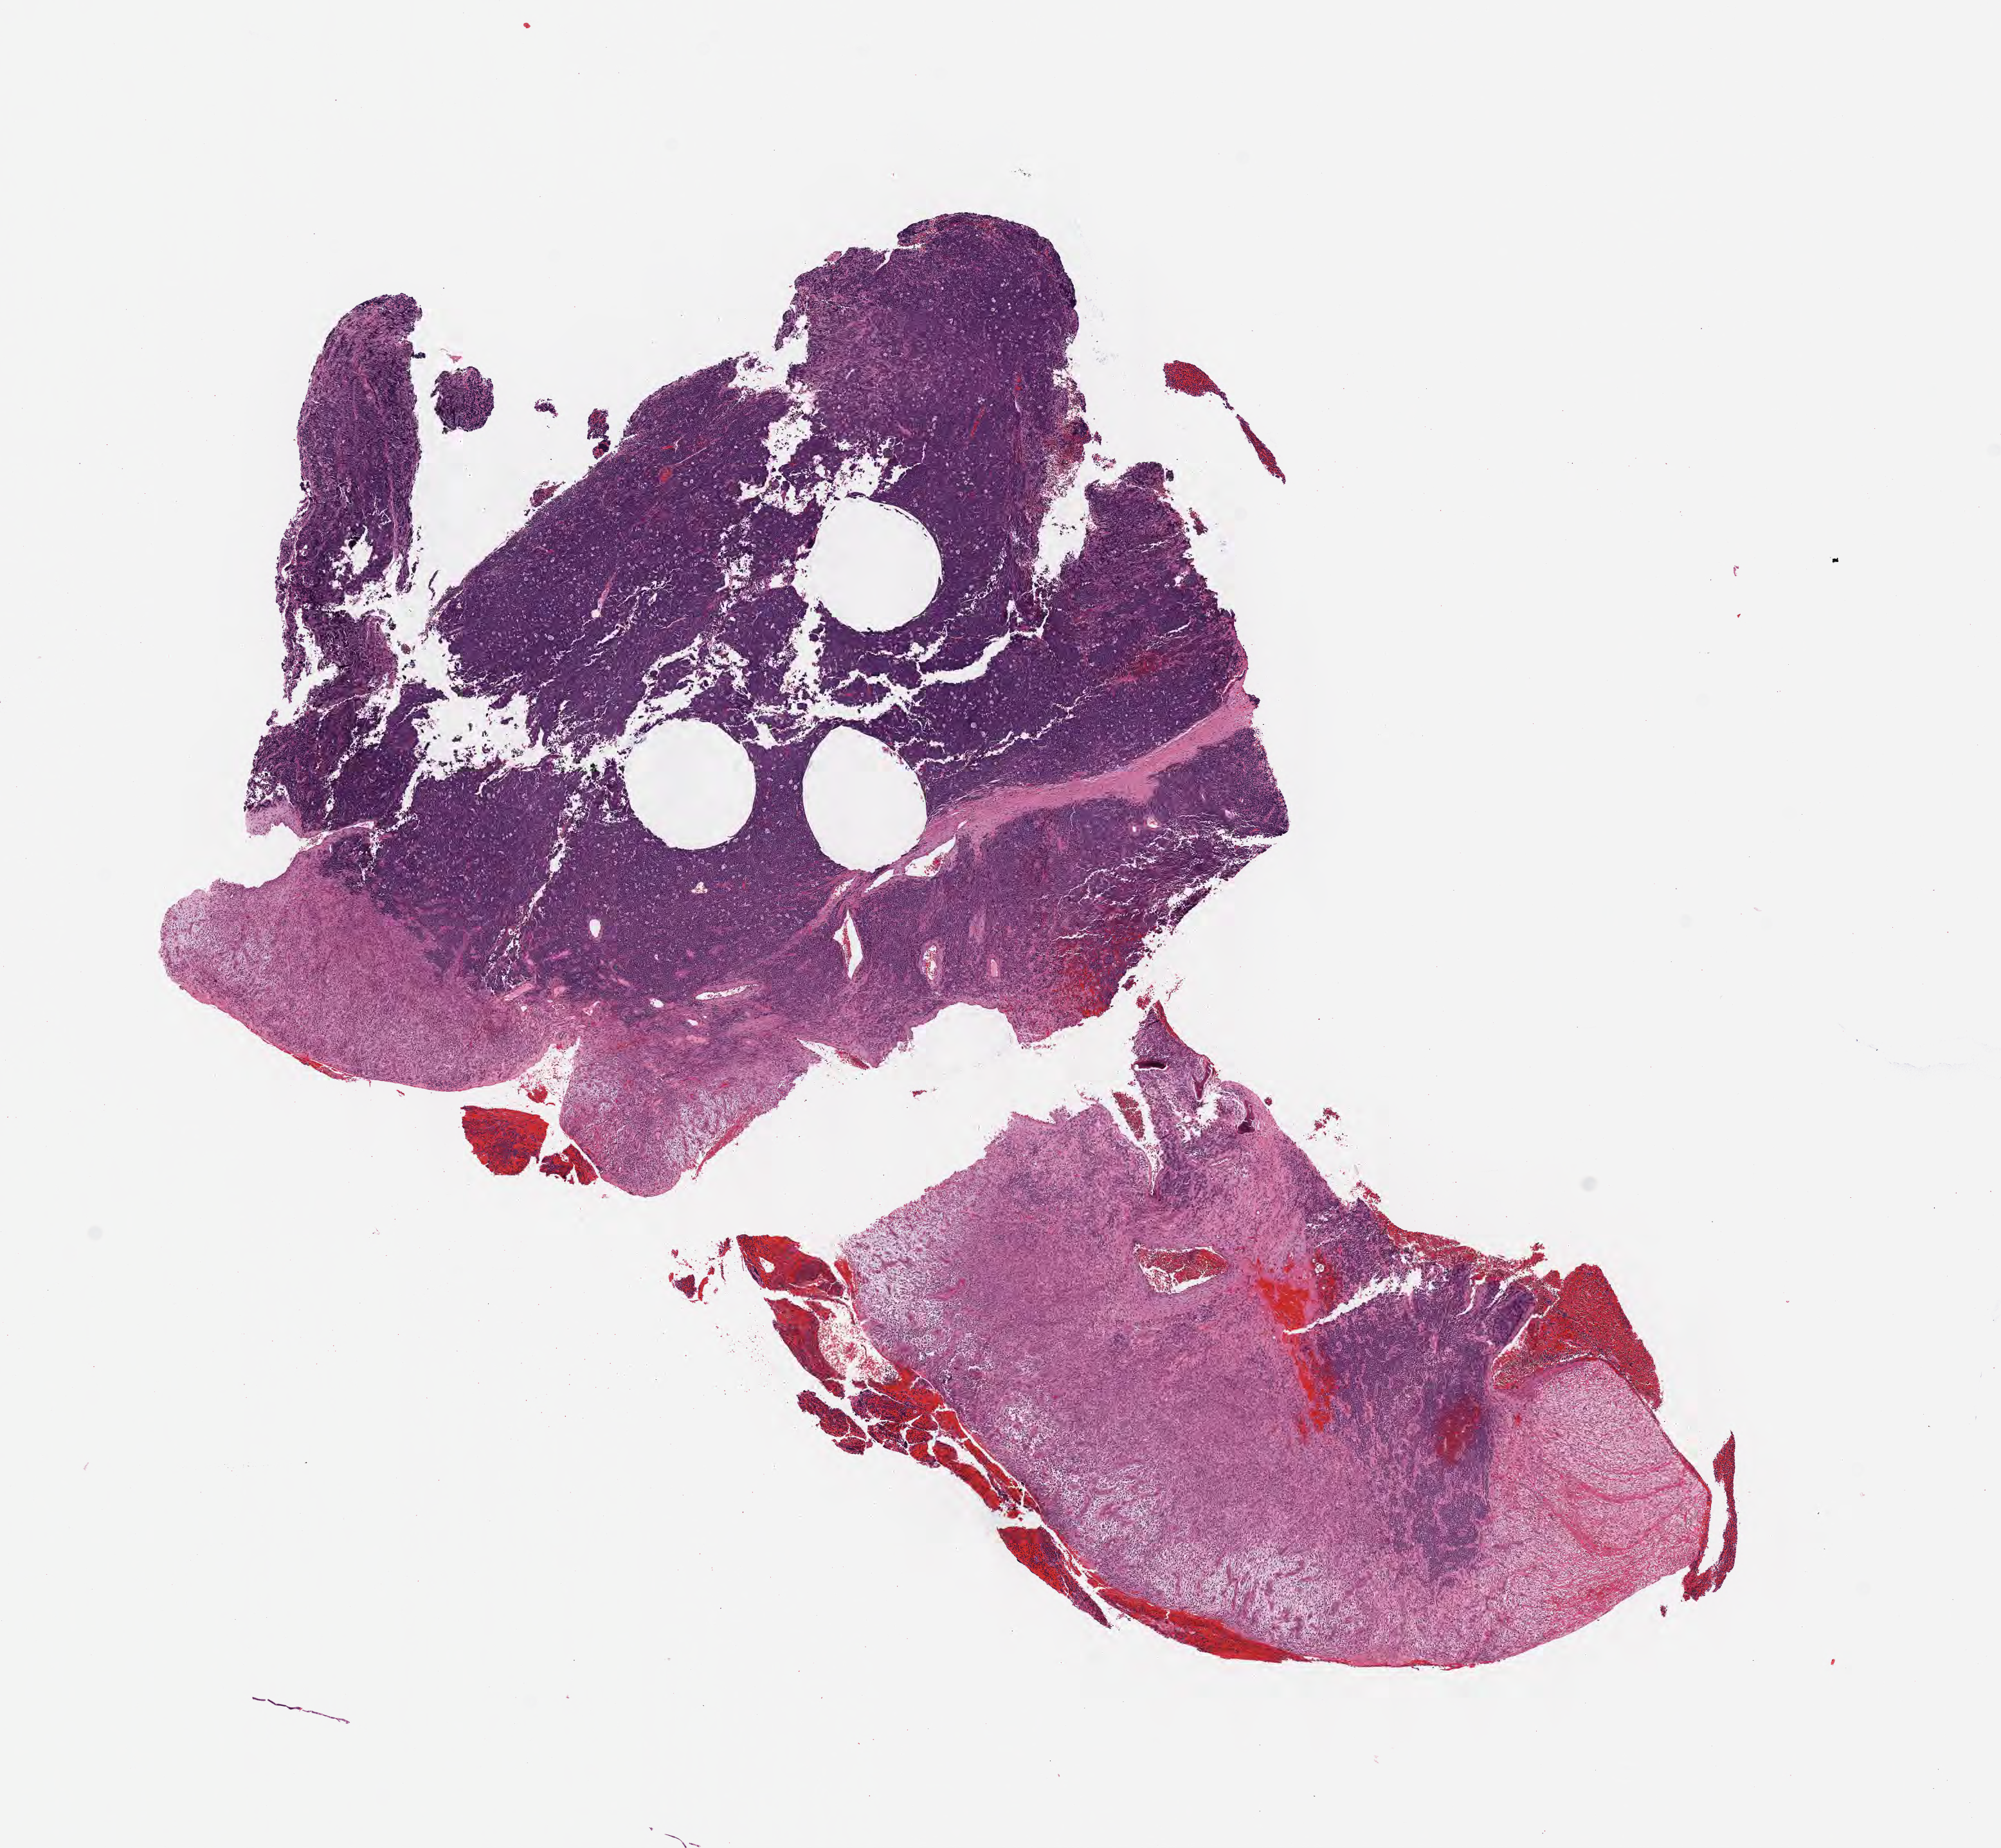
Whole-slide image, hematoxylin and eosin (H&E) stain, whole scanned area (about 12.6 x 11.6 mm) shown as a low-resolution overview, formalin-fixed paraffin-embedded section, primary tumor, site: mandible. Male patient; age at initial diagnosis 6 years. Pathologist review of this section (percent, as recorded): tumor cells 60%, tumor nuclei 85%, stromal cells 15%, necrosis 15%, normal cells 10%. Infiltration values recorded for this section: lymphocyte infiltration 50%, monocyte infiltration 20%, neutrophil infiltration 20%.
Ann Arbor stage (patient): Stage IV. Diagnosis: Burkitt lymphoma, NOS.